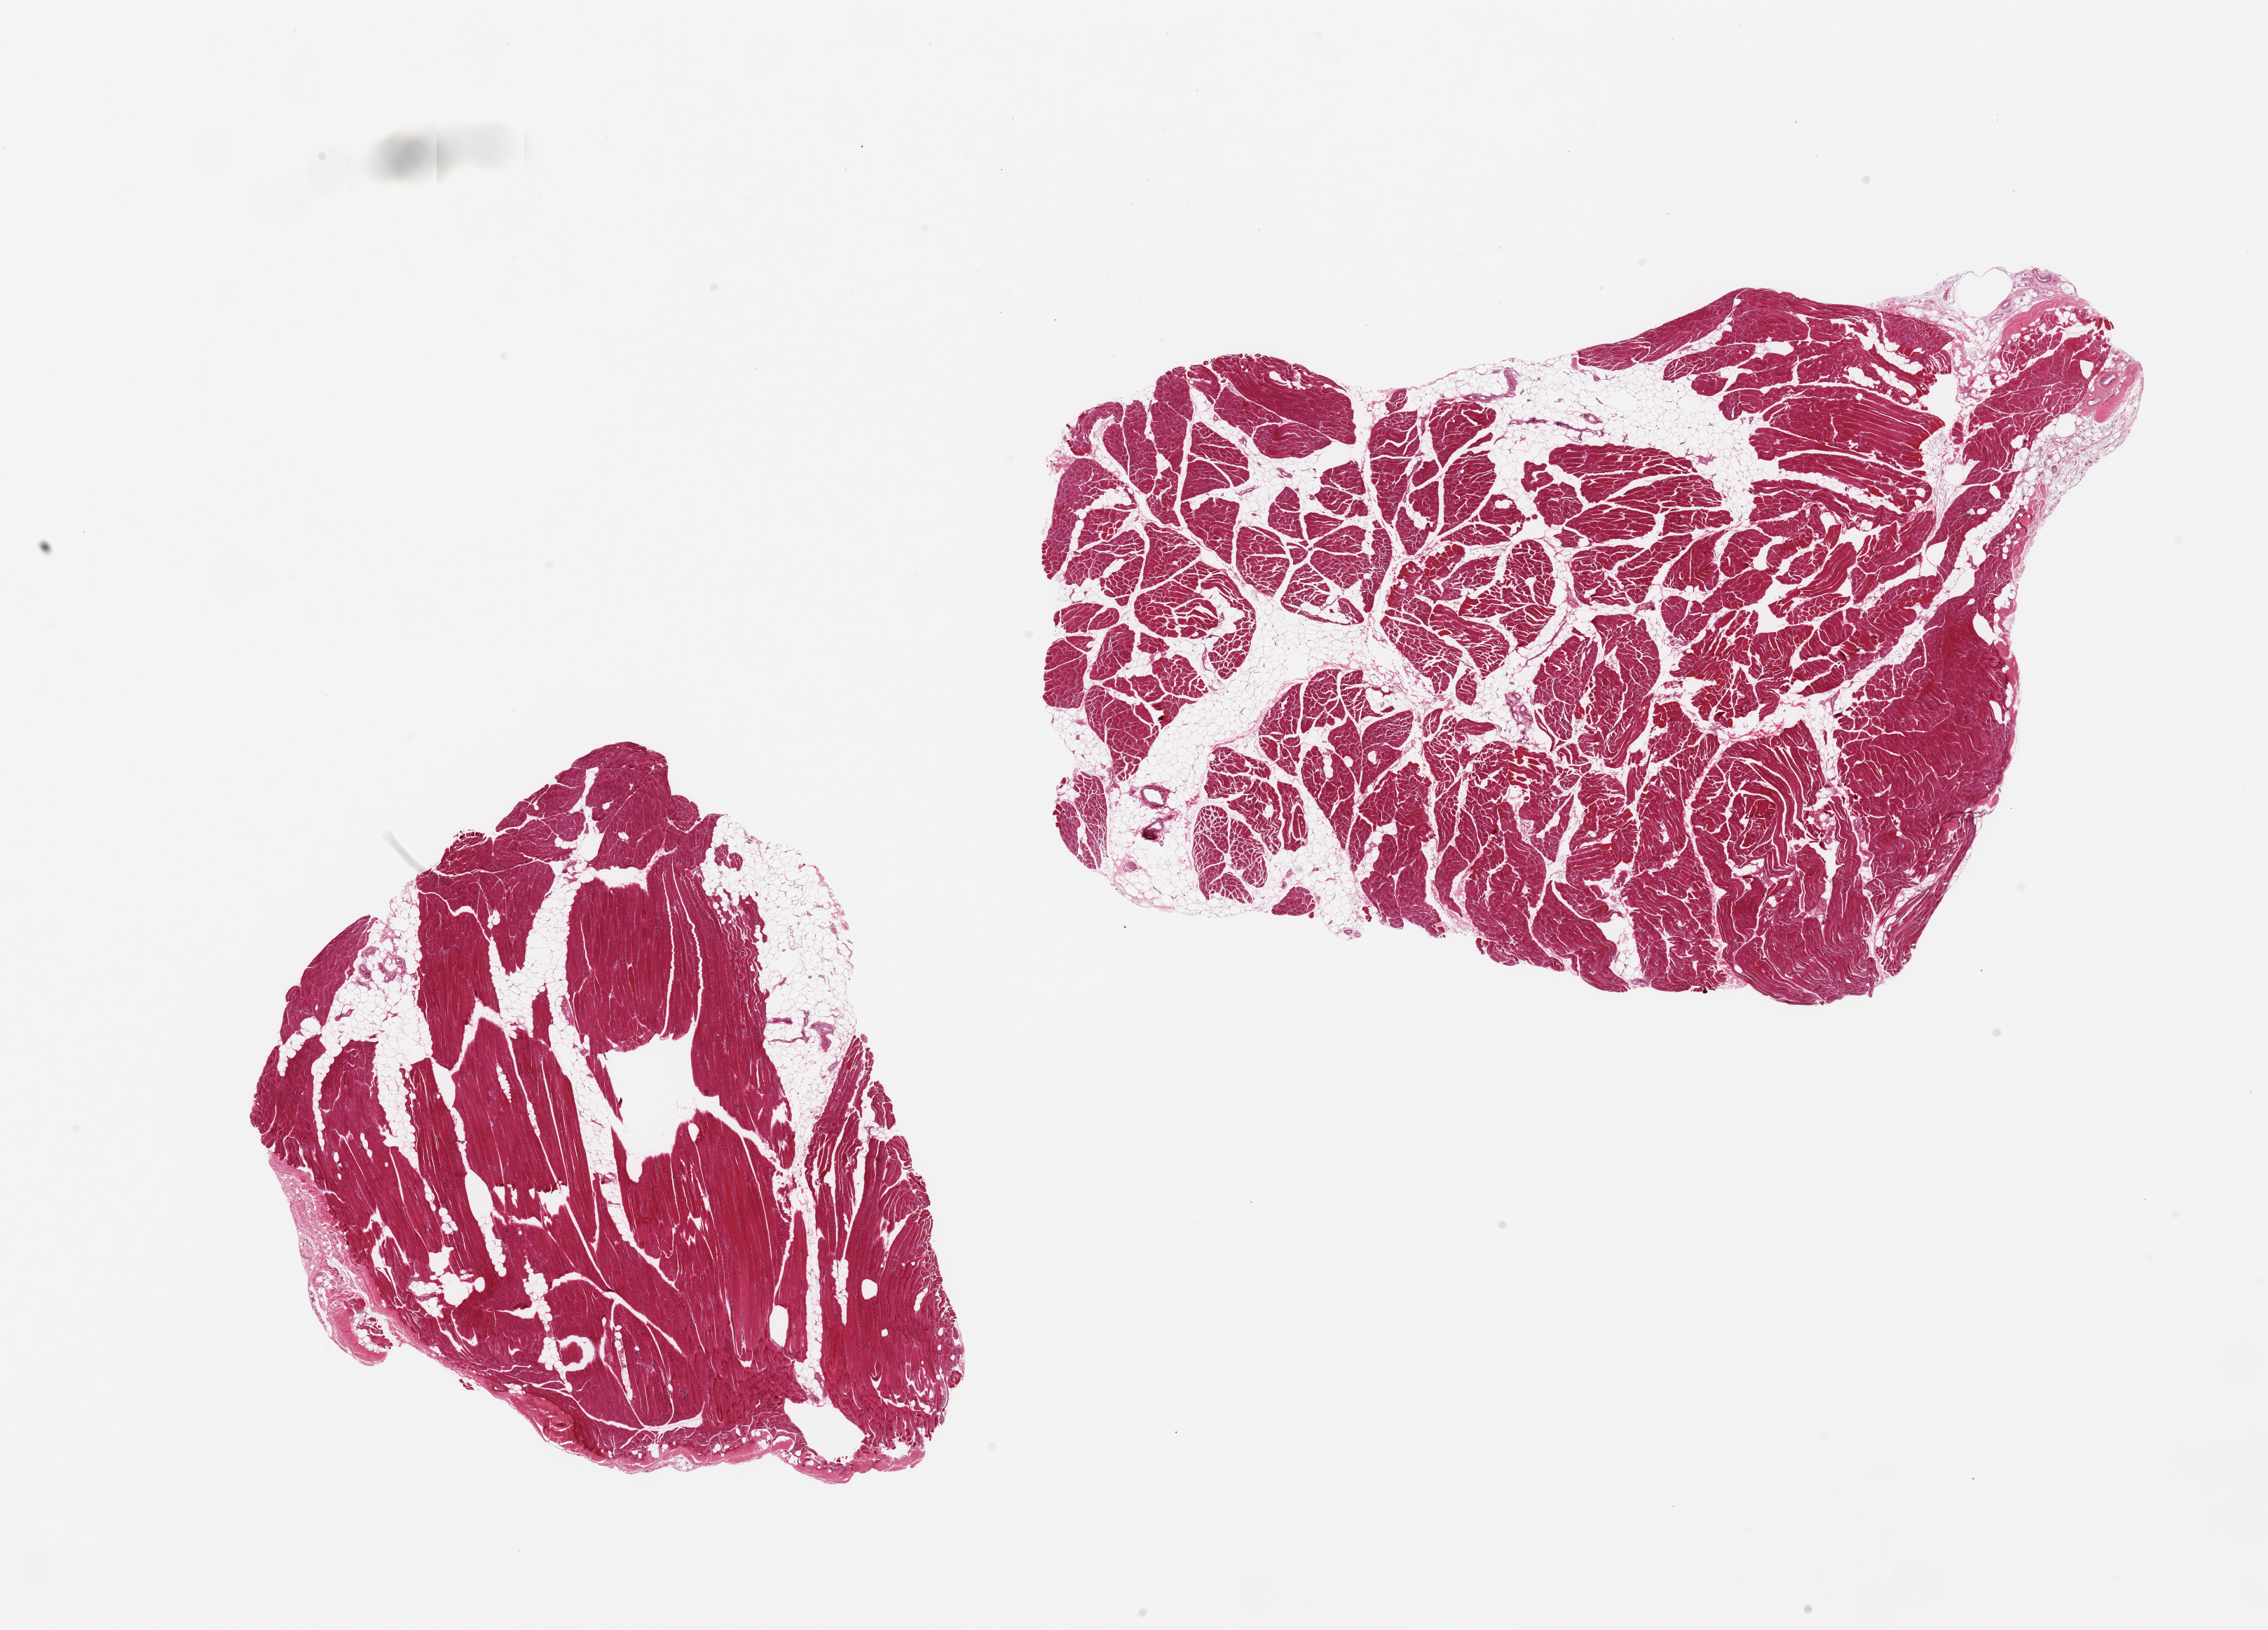
Whole-slide image, H&E stain — a low-resolution overview of the entire scanned area, about 25.6 x 18.4 mm, PAXgene-fixed, paraffin-embedded tissue, sampled site (target tissue): skeletal muscle, donor tissue sample. Donor sex: female.
- pathologist's review note for this sample: 2 pieces; 10% internal fat